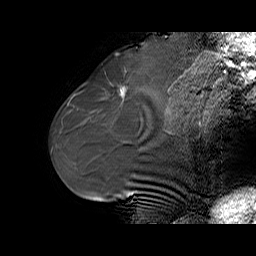
Breast MRI (dynamic contrast-enhanced), one sagittal slice. Slice 25 of 70 in the series (ordered by position). Dynamic contrast-enhanced series, time point 2 of 6 at this slice position (early post-contrast). 1.5 T. TE 5.5 ms, TR 32.9 ms. 256 × 256 image matrix. Female patient. Case-level facts recorded for this patient, not image findings: setting: breast cancer imaged before/during neoadjuvant chemotherapy; receptor status: HER2-positive.
Structures marked on this image (semi-automatic segmentation, software-assisted and operator-edited):
- analysis volume of interest (the breast-tissue region the enhancement analysis was run in; not a lesion): bounding box <97,73,141,114> (left, top, right, bottom; pixels)
- tumour enhancement mask (voxels above the 100 % enhancement threshold inside the analysis volume of interest): <120,89,124,96>